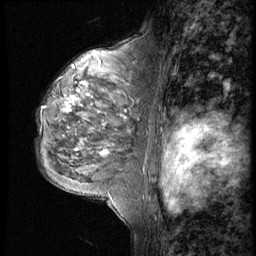
Breast MRI (dynamic contrast-enhanced), one sagittal slice; position 33 of 56 along the scan axis; 4 images stored at this slice position (order not interpretable as contrast timing); 1.5 T; TE 4.2 ms, TR 9 ms; 2.5 mm slice thickness; 256 × 256 image matrix. Patient: female, 50 years. From the clinical record (not read from this slice): setting: breast cancer imaged before/during neoadjuvant chemotherapy; receptor status: triple-negative.
Structures marked on this image (semi-automatically segmented with operator editing):
- analysis volume of interest (the breast-tissue region the enhancement analysis was run in; not a lesion): bounding box [x1, y1, x2, y2] px = [34, 46, 148, 188]
- tumour enhancement mask (voxels above the 140 % enhancement threshold inside the analysis volume of interest): [66, 98, 127, 157]